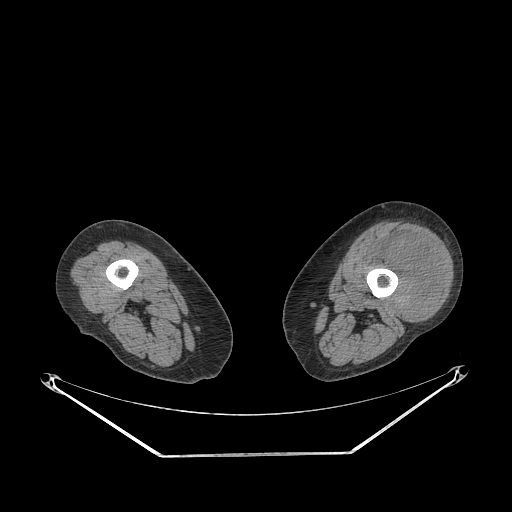
CT of an extremity soft-tissue mass (from a PET/CT study), one axial slice. Position 208 of 267 along the scan axis. Reconstruction kernel STANDARD. Soft-tissue window (W 400 / L 40 HU). 3.75 mm slice thickness. 512 × 512 image matrix, field of view 500 × 500 mm. Female patient. From the clinical record (not read from this slice): histological type: undifferentiated – high grade; grade: high; site of the primary tumour: left thigh.
Outlined on this slice (expert contour drawn on MRI and transferred to this co-registered scan by the dataset authors):
- gross tumour volume including surrounding oedema: bounding box (x1, y1, x2, y2) in pixels: (368, 233, 444, 318)
- gross tumour volume (mass): (383, 233, 442, 318)